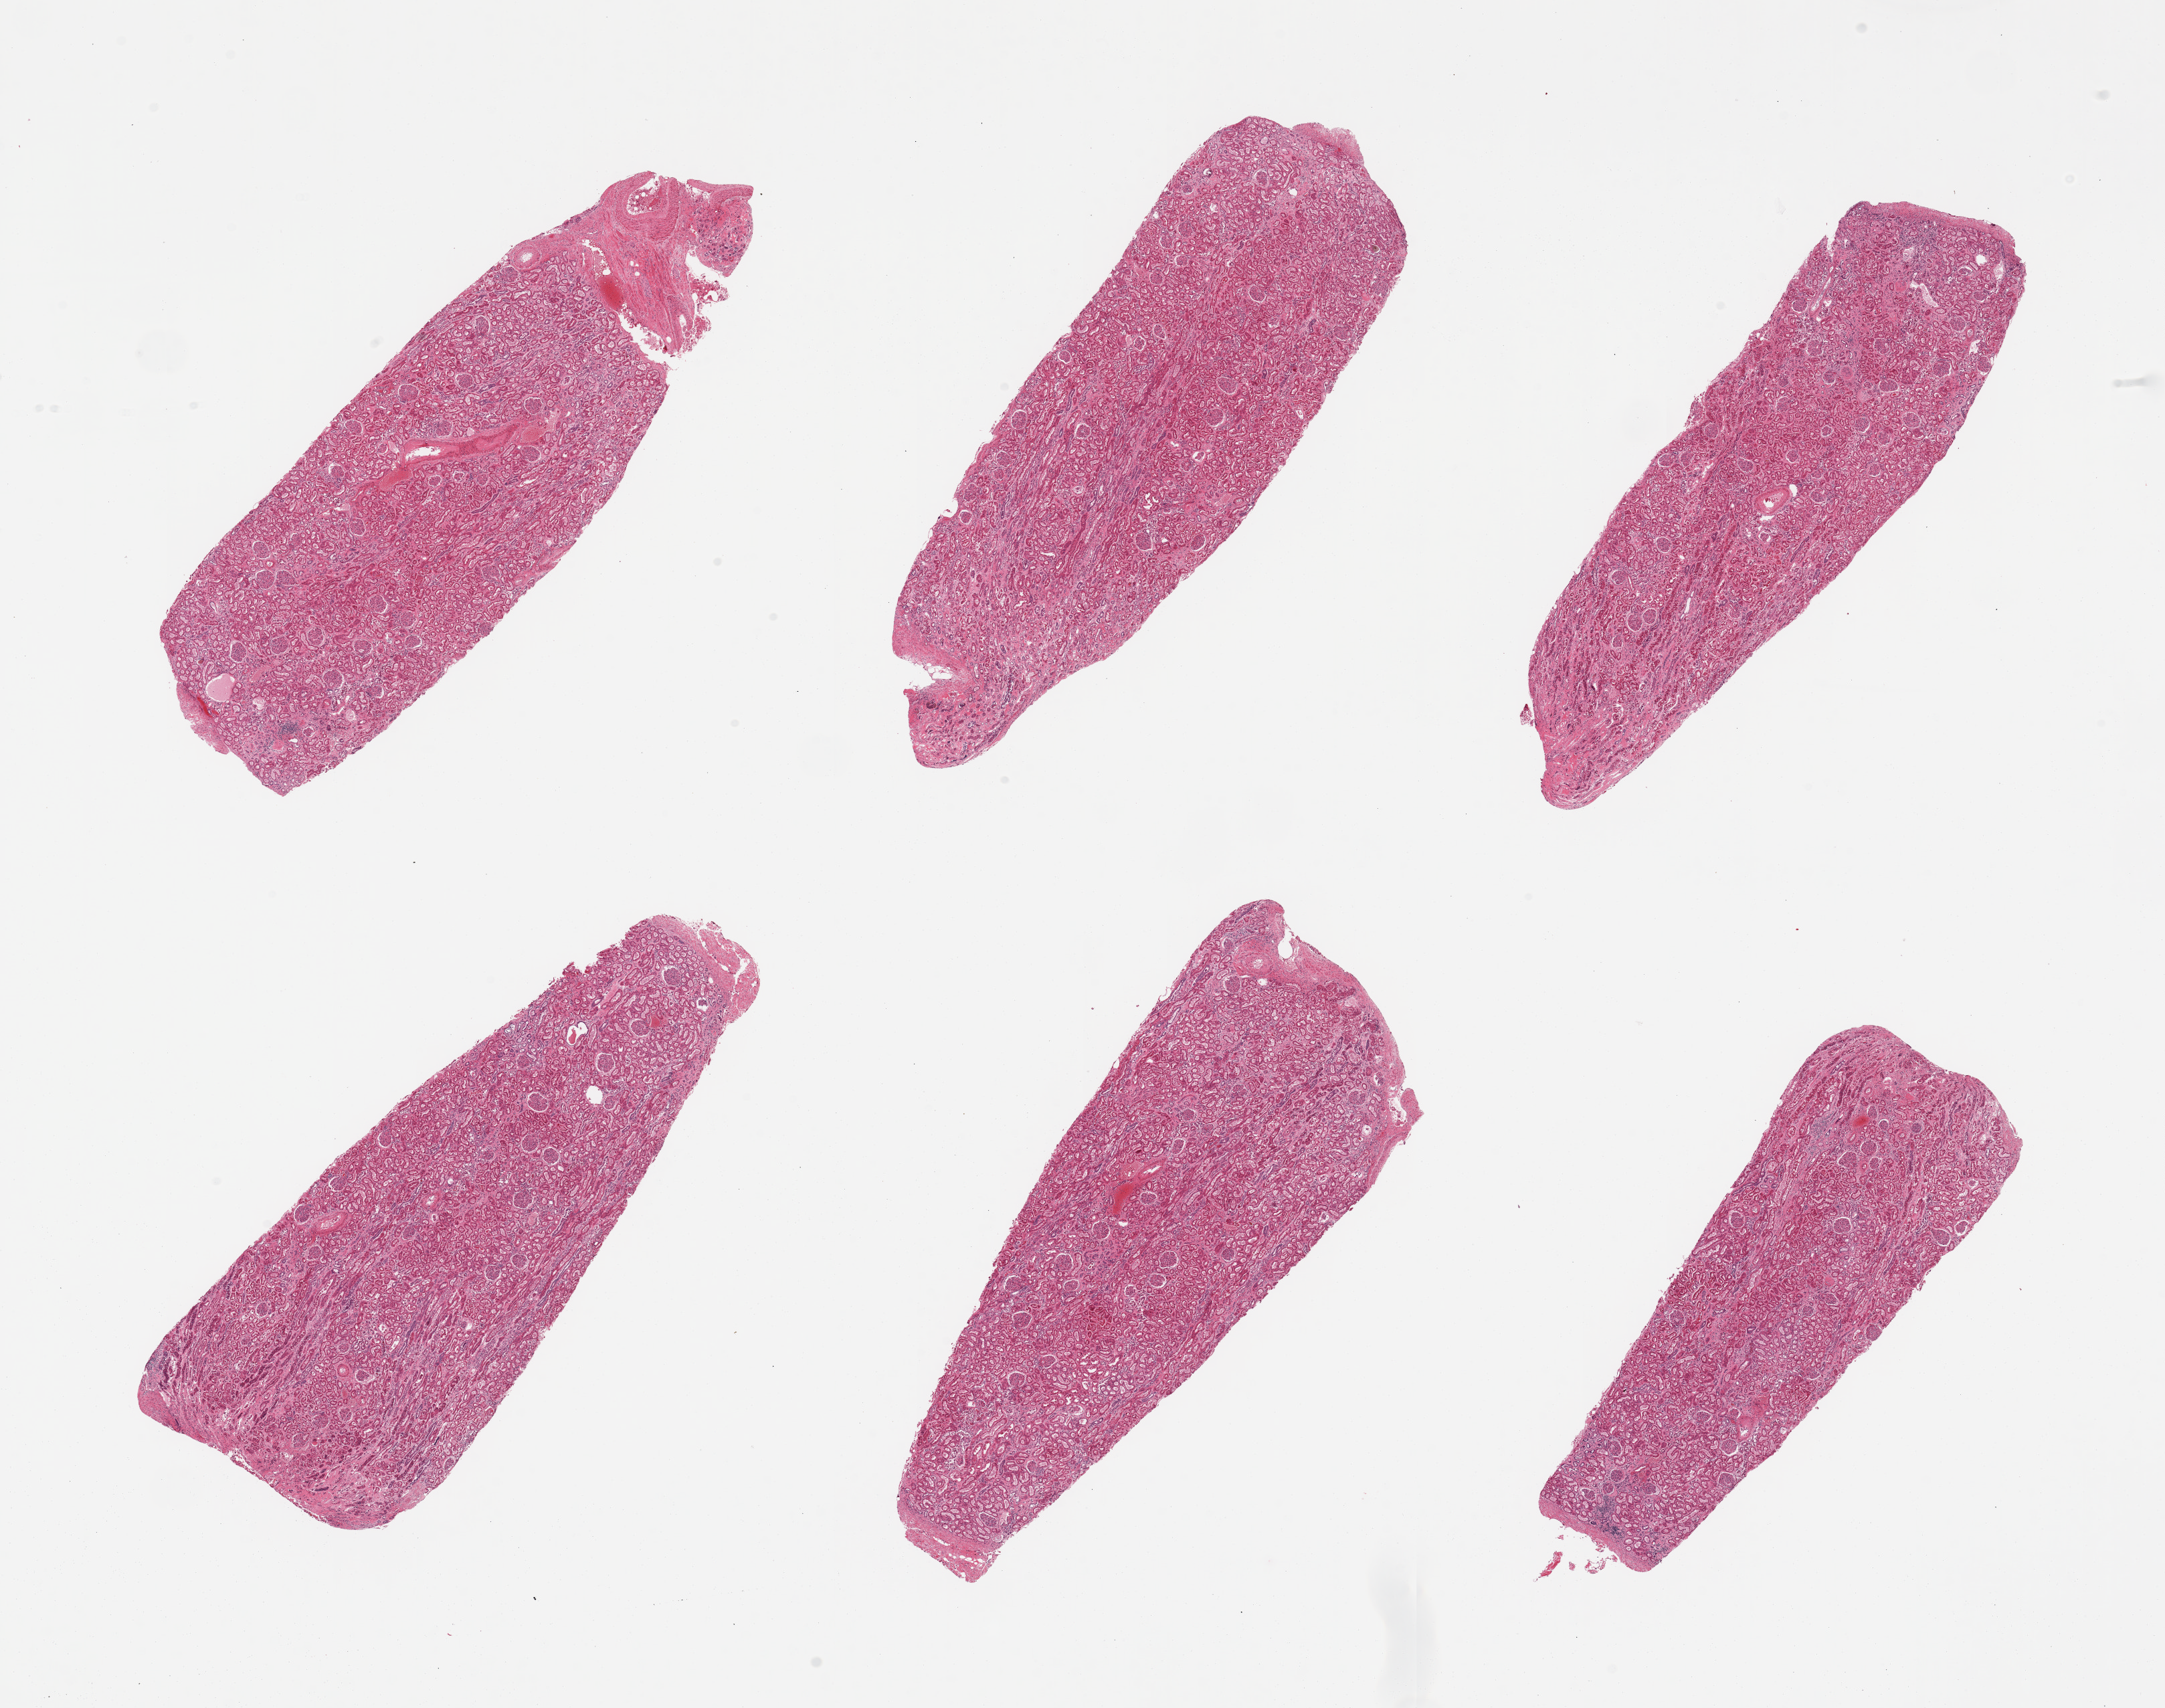
Whole-slide image, haematoxylin and eosin stain, shown as a low-resolution overview of the whole scanned area (about 25.6 x 20.2 mm, slide scanned at 20x), PAXgene-fixed paraffin-embedded (PFPE) section, target tissue: renal cortex, tissue donor sample. Donor sex: male.
Pathologist's review note for this sample: 6 pieces; occasional sclerosed glomerulus; moderate arterial sclerosis.